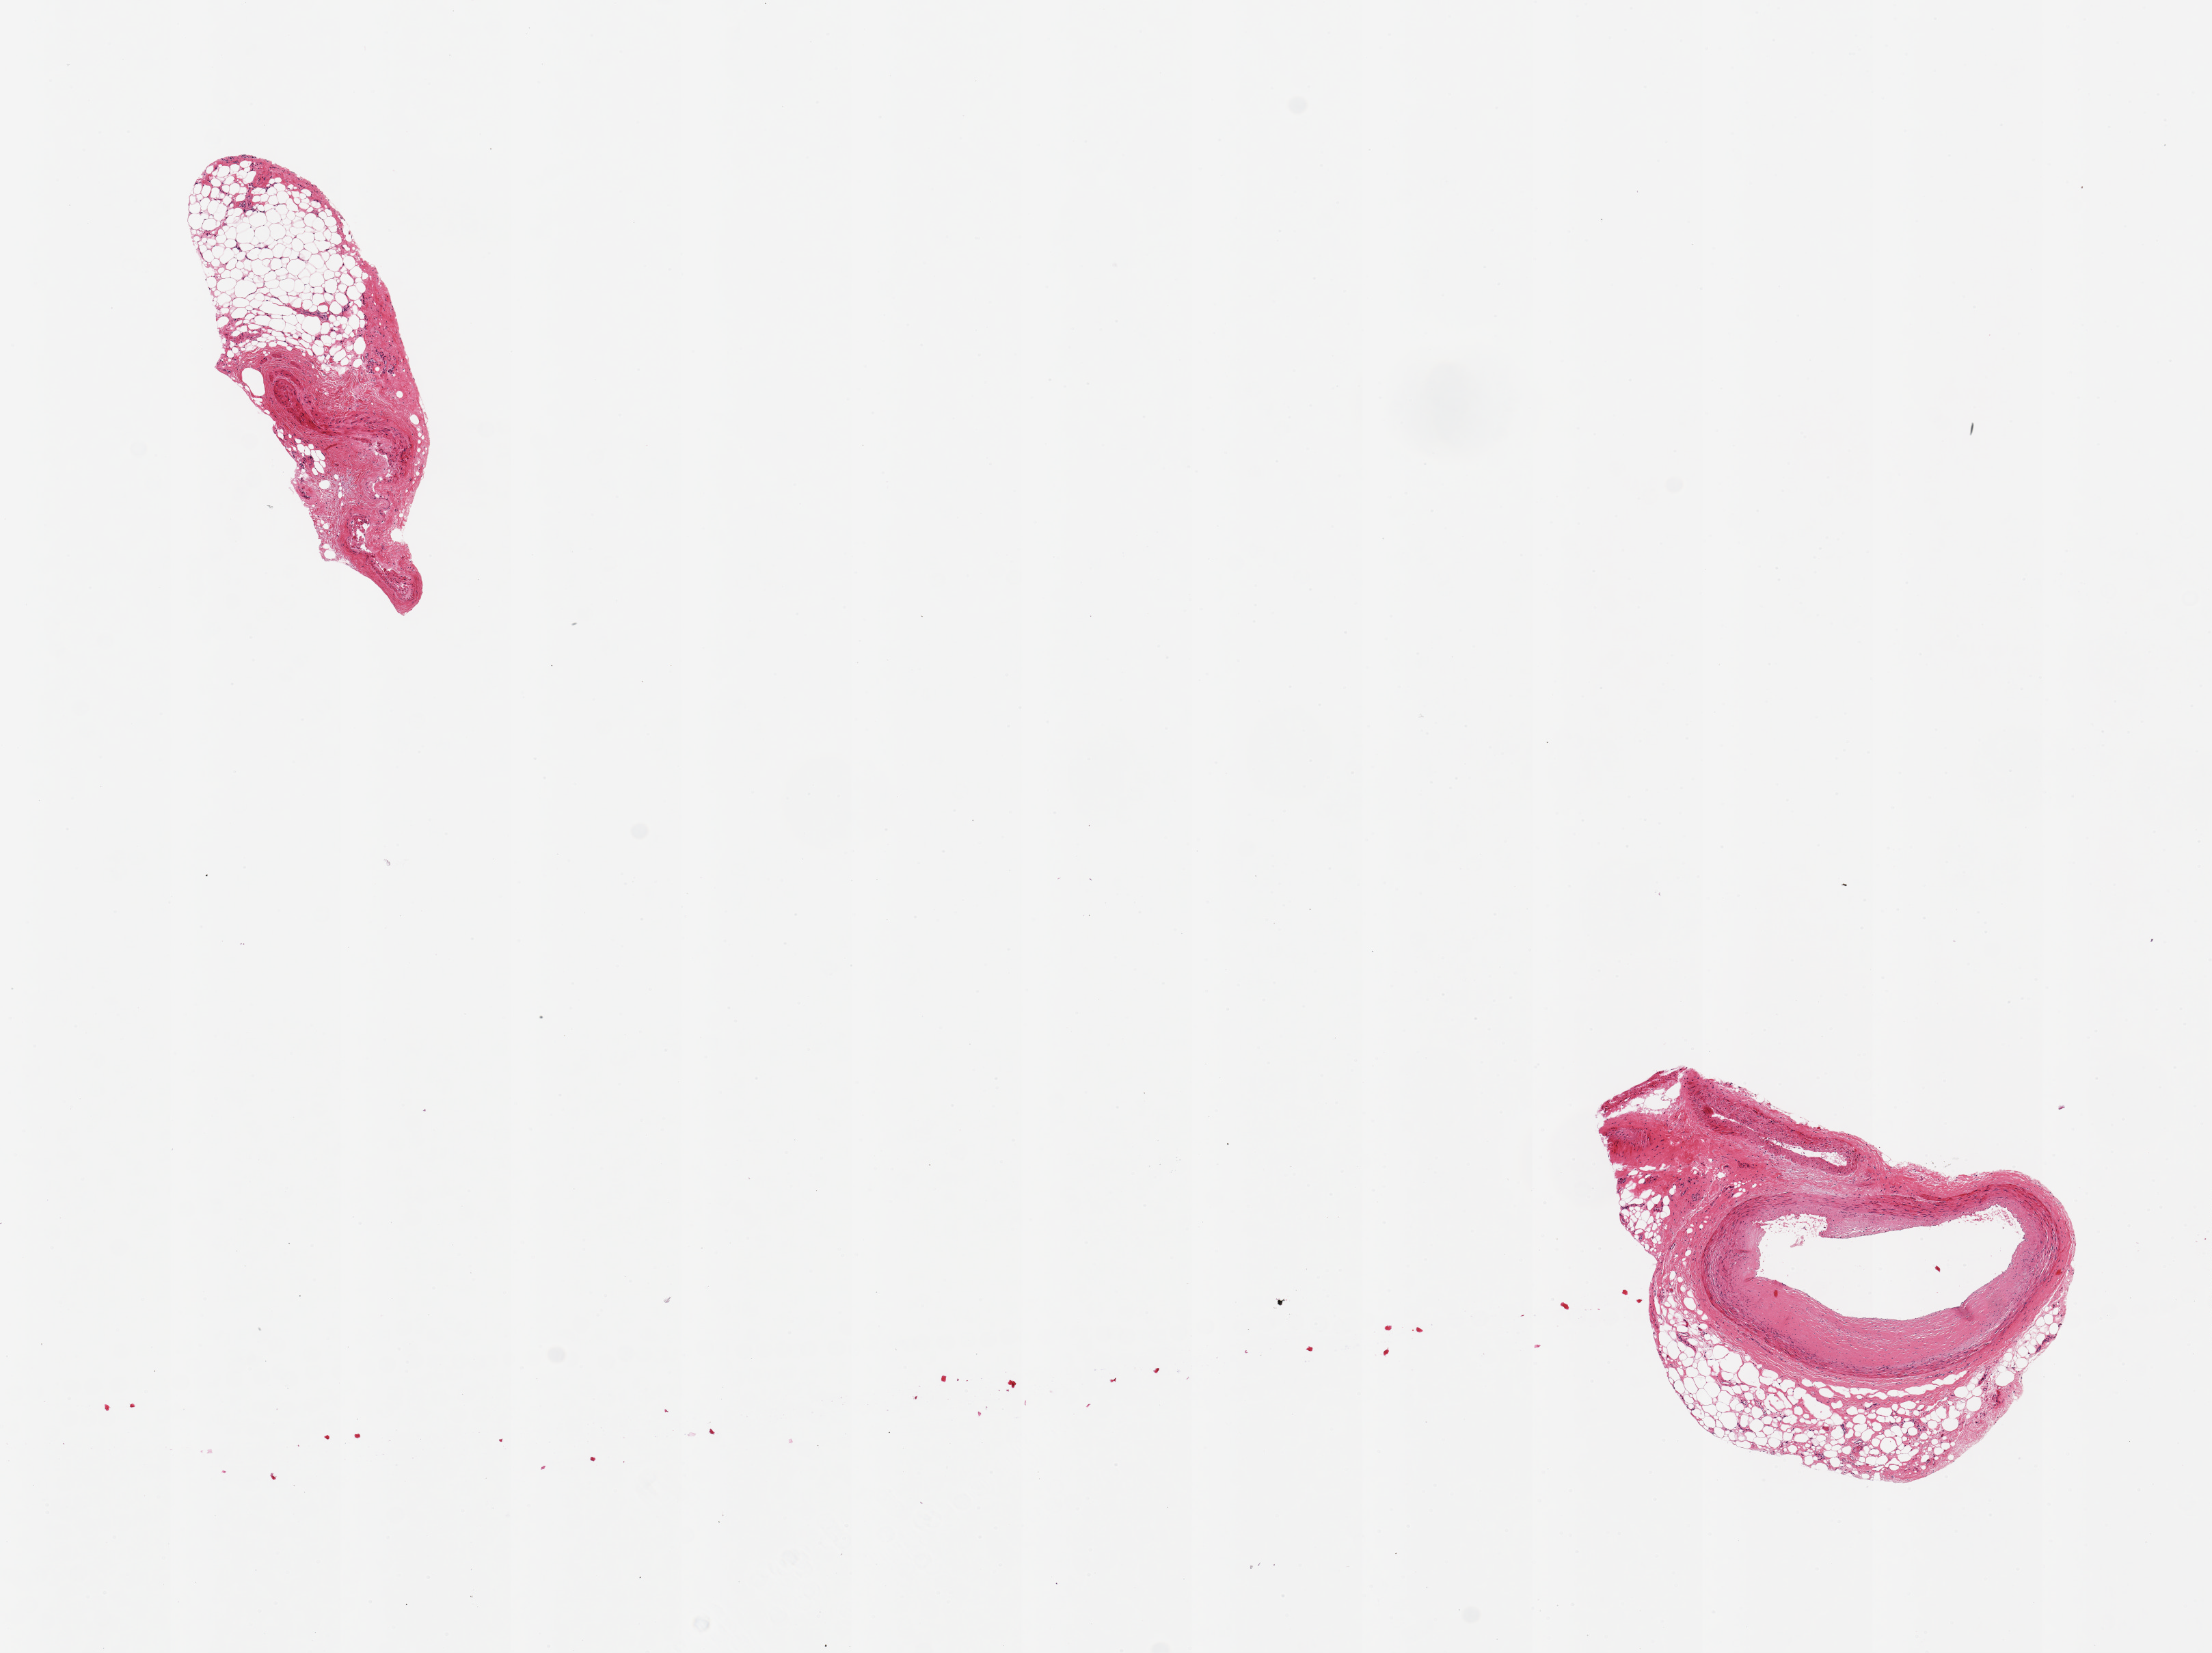
Haematoxylin and eosin whole-slide image, brightfield, whole scanned area (about 12.8 x 9.6 mm, from a 20x scan) shown as a low-resolution overview, PAXgene-fixed, paraffin-embedded tissue, target tissue: coronary artery, donor tissue sample. Male donor.
- review note (as recorded): 2 pieces, 3x1 & 3x2mm; larger piece is 40% occluded, 2mm atheromatous artery with ~30% peripheral adipose and a small tributary; smaller piece is ~90% fibroadipose and a very small 0.6 mm artery